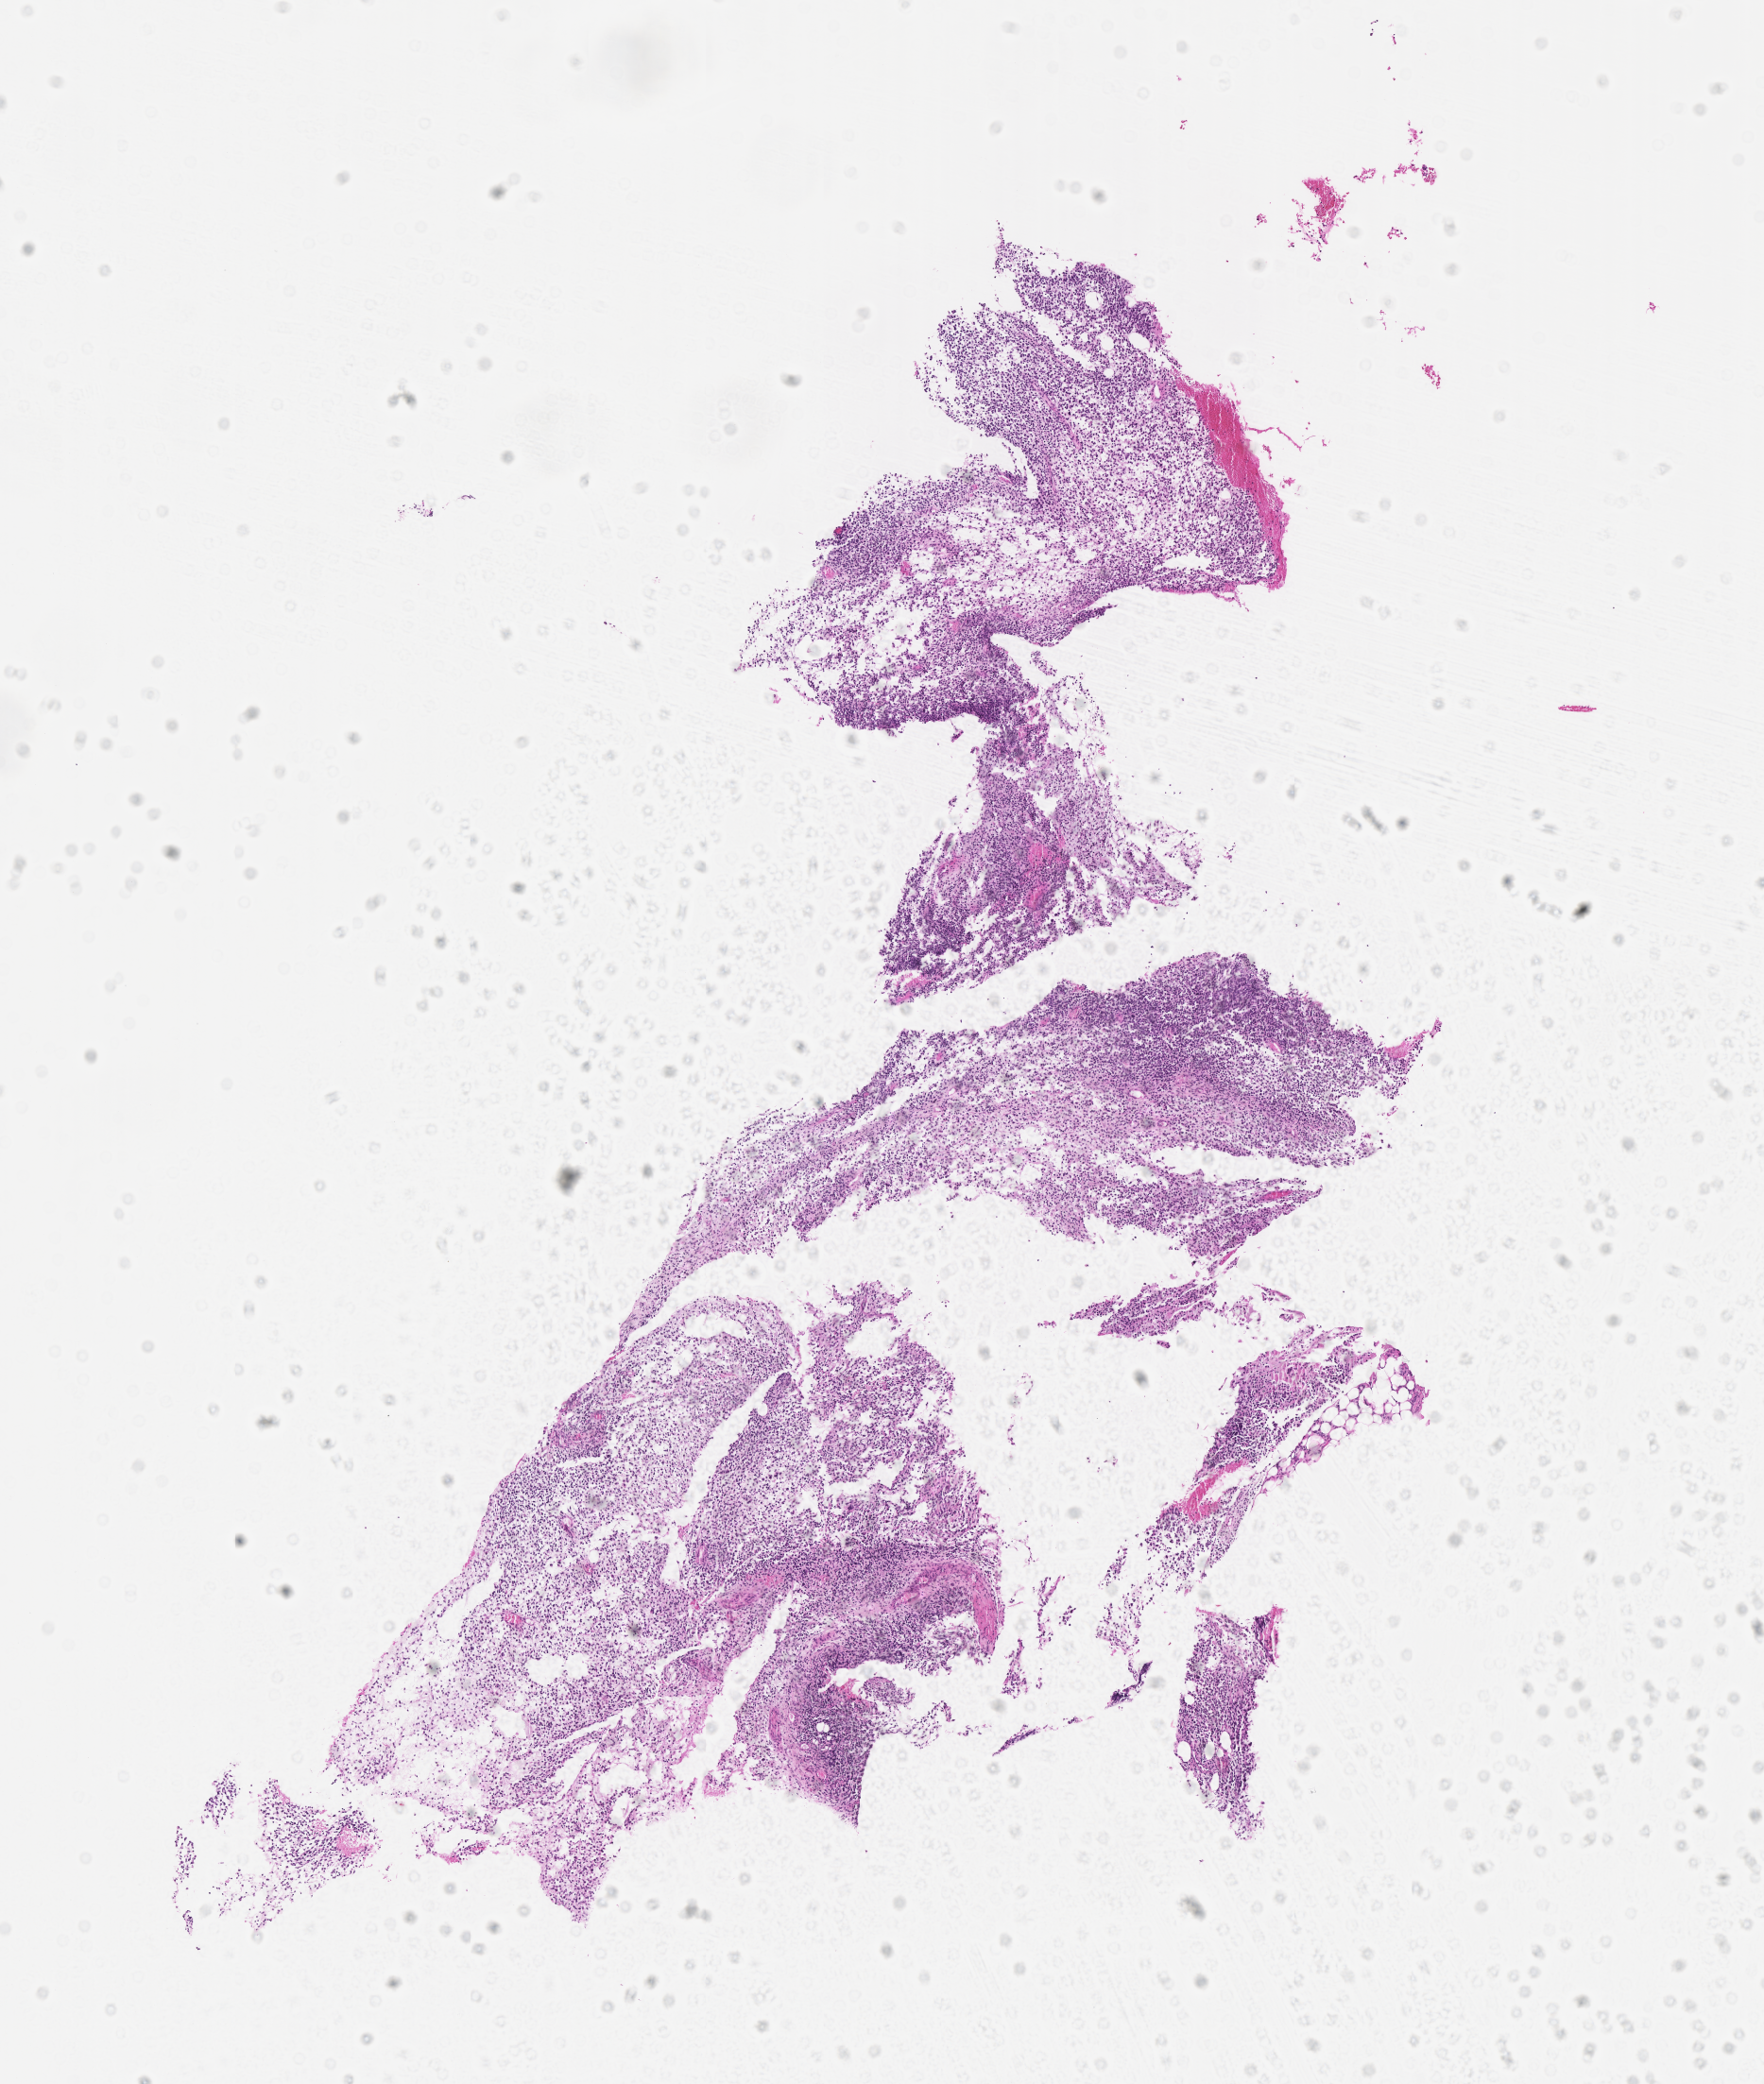
Haematoxylin and eosin whole-slide image of tumor tissue — low-resolution overview of the scanned area, about 7.5 x 8.9 mm; formalin-fixed, paraffin-embedded (FFPE) tissue; site: abdomen. Patient: female, age 1.6 years at diagnosis.
Stage (as recorded): 3. Diagnosis: rhabdomyosarcoma; histological classification: embryonal rhabdomyosarcoma. Primary site (case record): pelvis, site indeterminate.